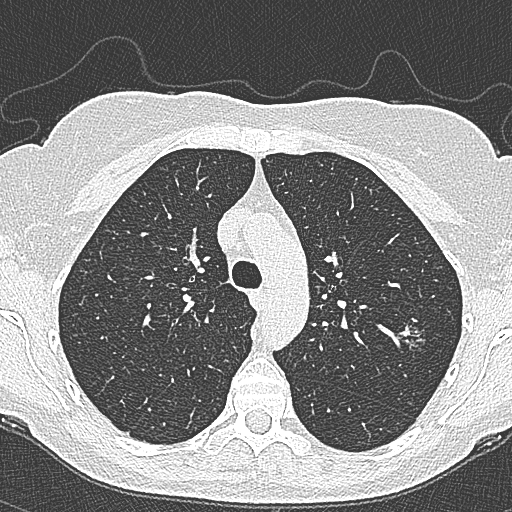
Low-dose screening chest CT, axial slice. Second annual screen. Lung window (W 1500 / L -600 HU). 512 × 512 image matrix. Female participant, aged 65 years at enrolment.
Expert-annotated lung lesion, bounding box (x1, y1, x2, y2) in pixels: (392, 309, 437, 355). The screening reader recorded 4 non-calcified nodules or masses ≥4 mm on this exam (left upper lobe, left upper lobe, left upper lobe, right lower lobe); which of them this box marks is not recorded. Official screen result: positive, change unspecified: nodule(s) >= 4 mm or enlarging nodule(s), mass(es), or other non-specific abnormalities suspicious for lung cancer. Lung cancer was diagnosed 54 days after this screen: bronchiolo-alveolar carcinoma, non-mucinous, left upper lobe, stage IA (AJCC 6th edition), 10 mm at pathology.